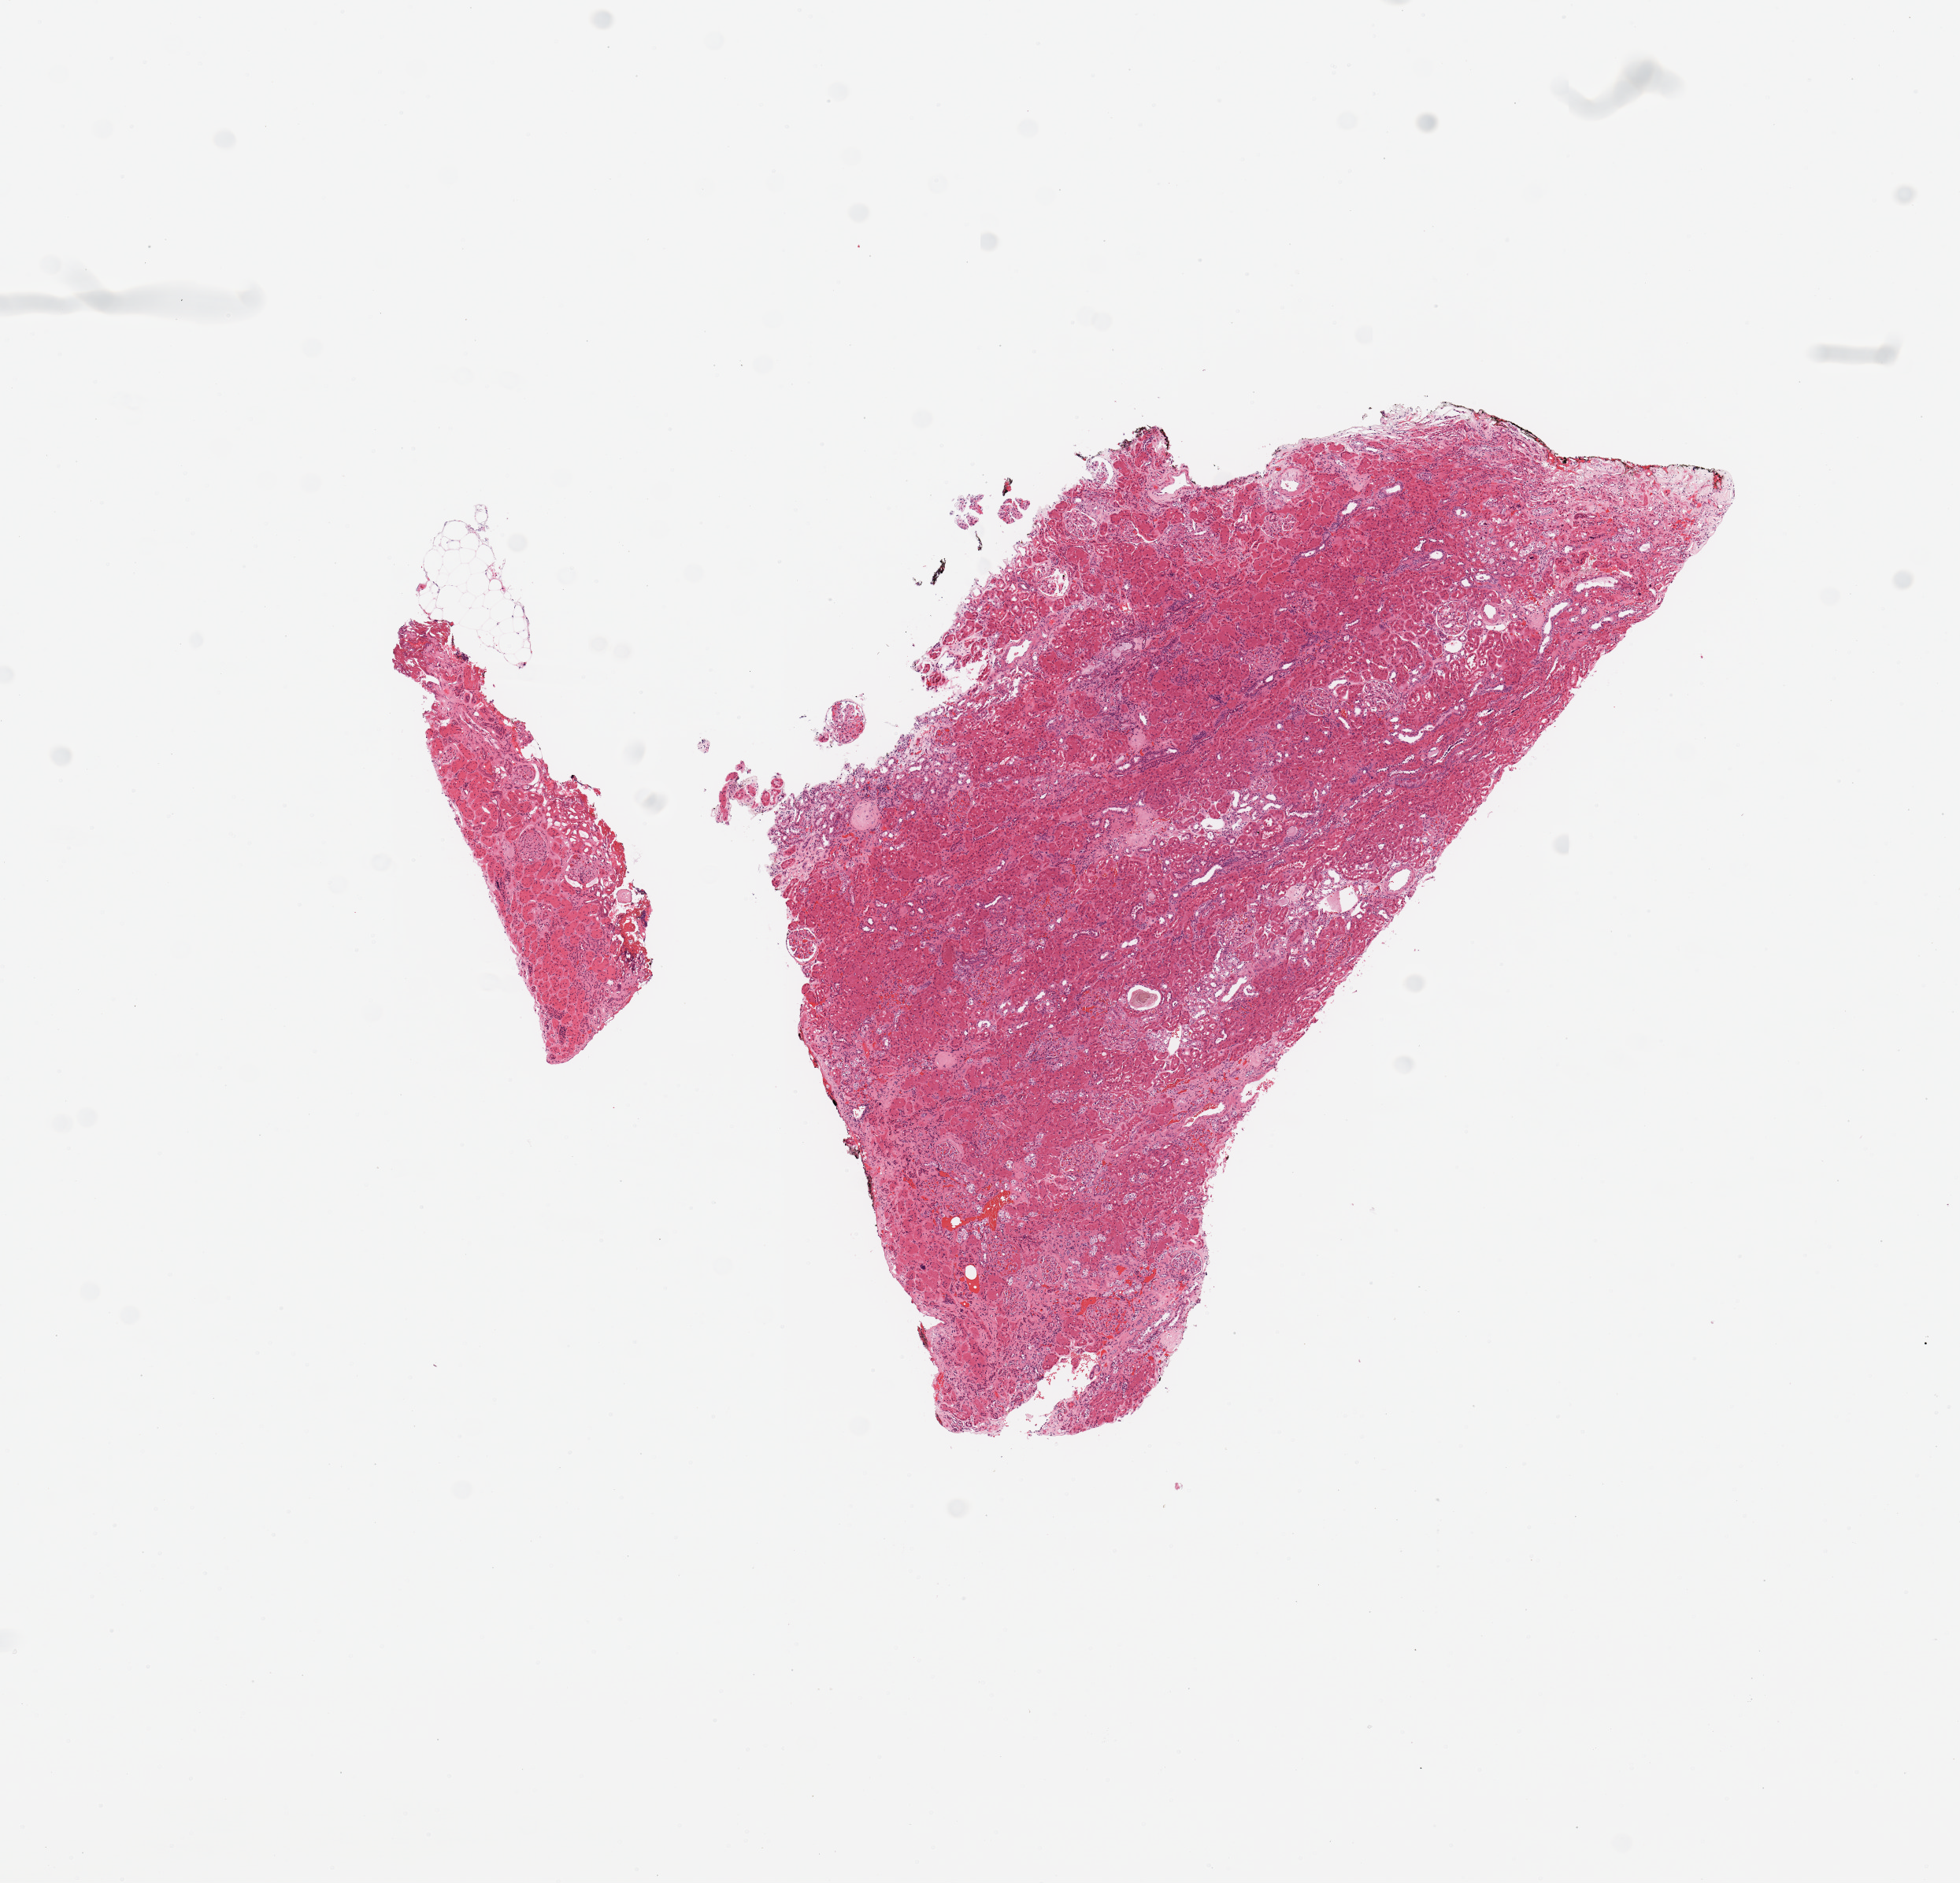
Whole-slide histology image, H&E — shown as a low-resolution overview of the whole scanned area (about 9.8 x 9.5 mm, acquisition: 20x scan). Normal (non-tumour) tissue sample, sampled site: kidney. Male, 57 y/o.
This section: normal (non-tumour) tissue from the same patient. Patient diagnosis: Renal cell carcinoma, NOS.